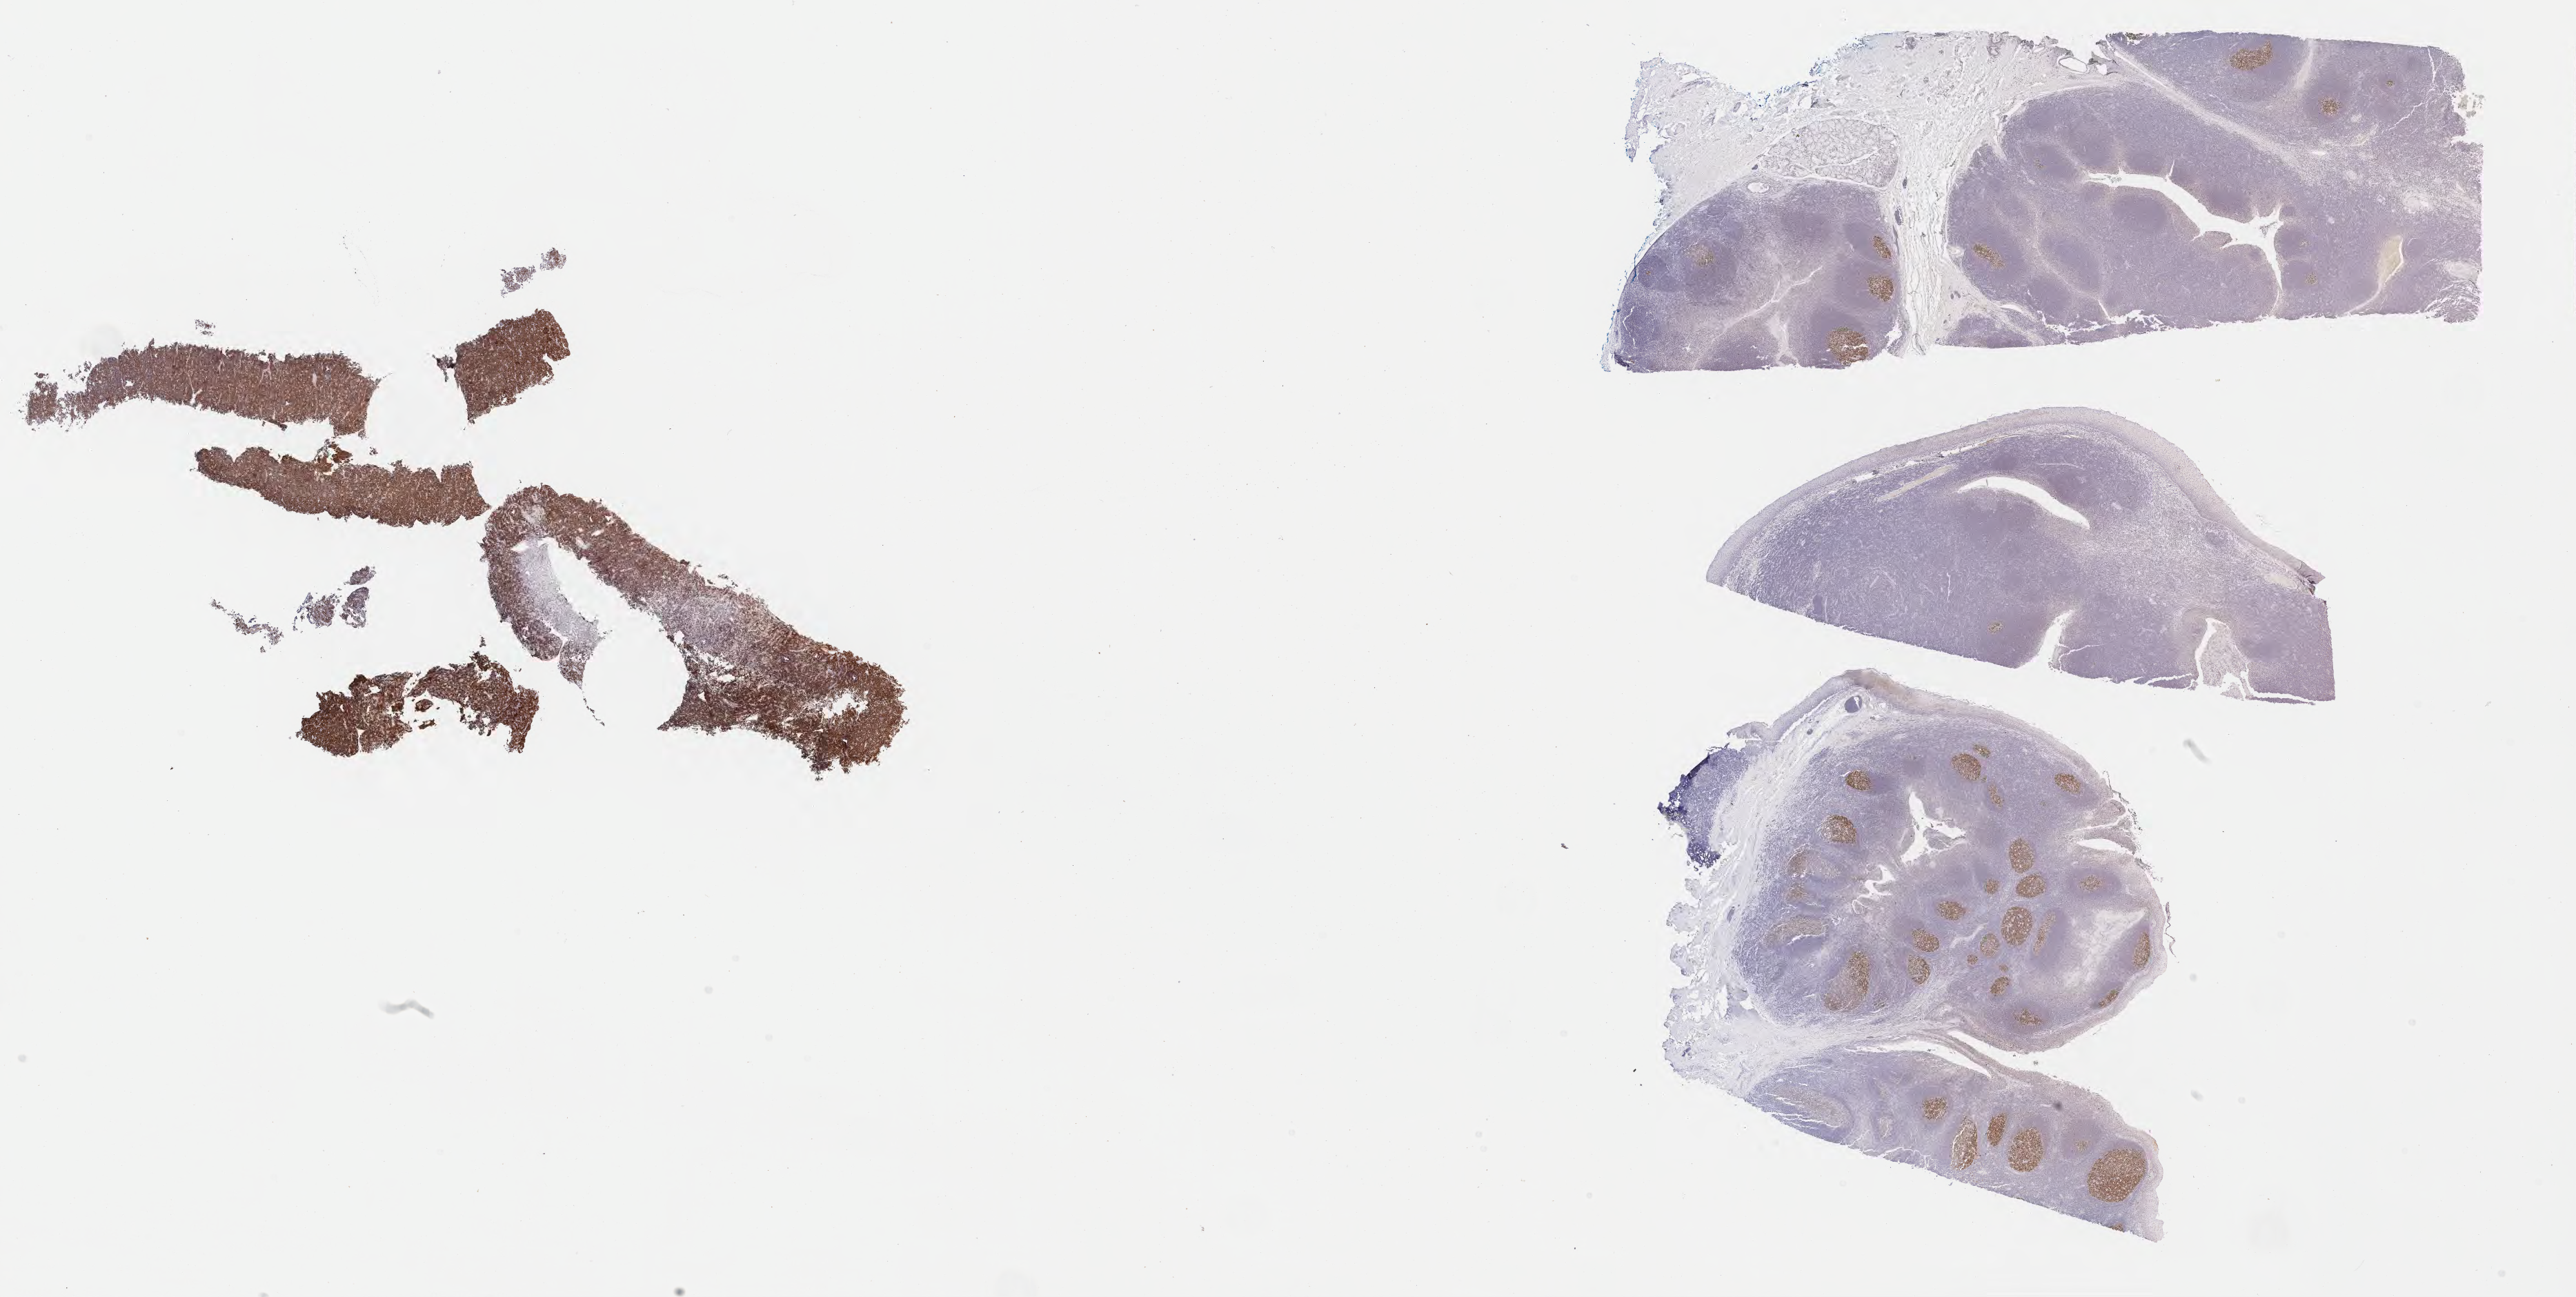
IHC for BCL6, whole-slide image, shown as a low-resolution overview of the whole scanned area (about 30.2 x 15.2 mm); specimen: tumor tissue; site: liver. Male patient; age at initial diagnosis 4 years.
Diagnosis: Burkitt lymphoma, NOS.